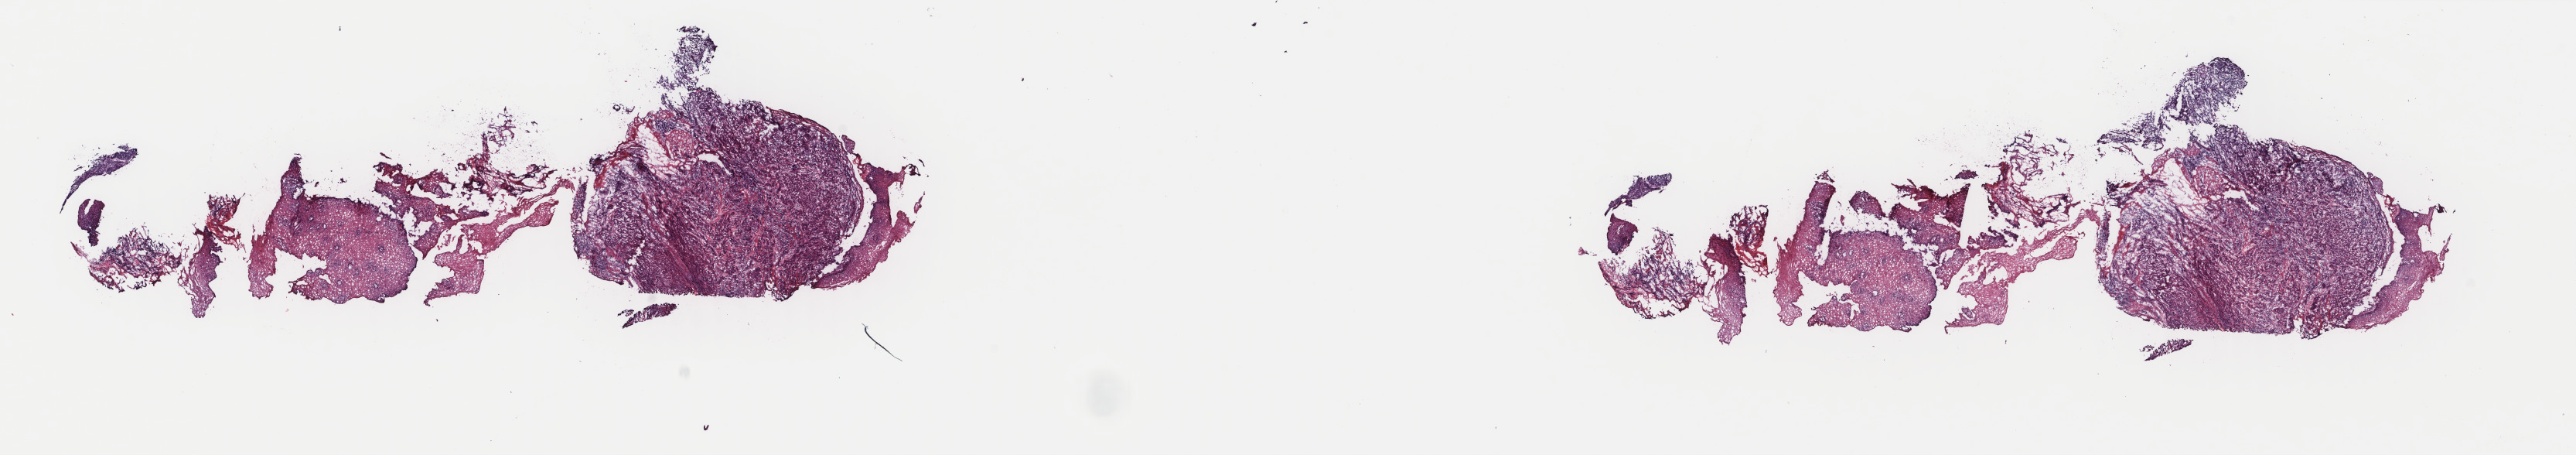
Whole-slide histology image, H&E, low-resolution overview of the scanned area, about 26.4 x 4.7 mm. Frozen section from the top of the tissue portion. Sample: primary tumour, esophagus. Patient: male, age at initial diagnosis 82 years. Histologic grade: GX (grade cannot be assessed). Pathologist review of this section (percent, as recorded): tumour cells 70%, tumour nuclei 60%, normal cells 30%, stromal cells 0%, necrosis 0%. Infiltration values recorded for this section: lymphocyte infiltration 0%, monocyte infiltration 0%, neutrophil infiltration 0%.
• pathologic diagnosis: Squamous cell carcinoma, NOS (middle third of esophagus)
• AJCC pathologic stage: IA (7th edition)